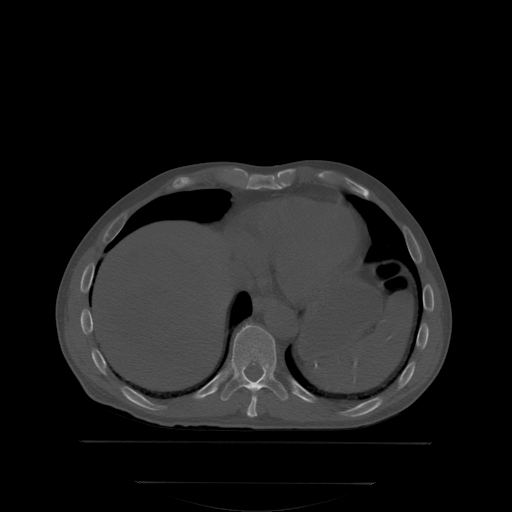
CT including the spine, one axial slice. Slice 195 of 350 in the series (ordered by position). Bone window (W 1800 / L 400 HU). 2.5 mm slice thickness. 512 × 512 image matrix, field of view 500 × 500 mm. Patient: male, 58 years. From the clinical record (not read from this slice): primary cancer: prostate.
Outlined on this slice (semi-automatic segmentation, software-assisted and operator-edited):
- T10 vertebra: bounding box (x1, y1, x2, y2) in pixels: (221, 323, 288, 401)
- T9 vertebra: (247, 391, 257, 416)